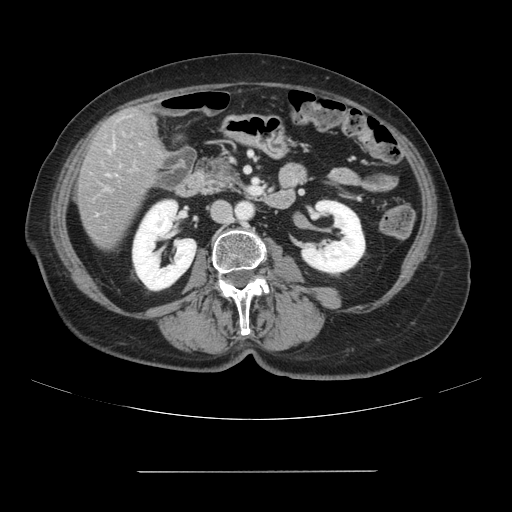
Contrast-enhanced abdominal CT, one axial slice. Position 22 of 111 along the scan axis. Intravenous contrast given. Soft-tissue window (W 400 / L 40 HU). 2.5 mm slice thickness. 512 × 512 image matrix, field of view 400 × 400 mm. Female patient, age 74 years. From the clinical record (not read from this slice): diagnosis: colorectal cancer liver metastases, imaged before liver resection.
Annotated regions visible in this slice (expert manual segmentation):
- liver: bounding box [x1, y1, x2, y2] px = [77, 106, 166, 249]